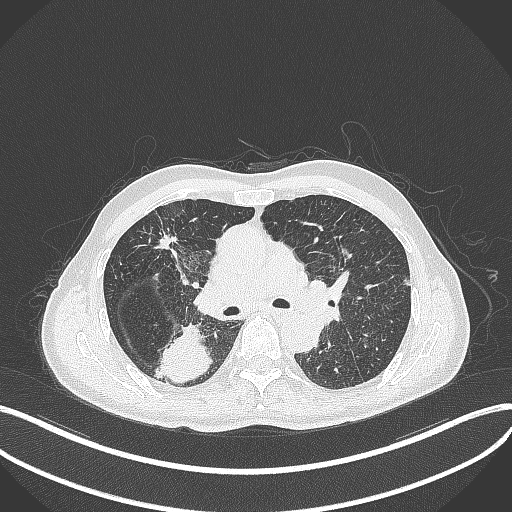
Chest CT, one axial slice. Slice 275 of 428 in the series (ordered by position). Reconstruction kernel B70f. 120 kVp. Lung window (W 1500 / L -600 HU). 512 × 512 image matrix, field of view 400 × 400 mm. Patient: male, 79 years. Case-level facts recorded for this patient, not image findings: clinical TNM (as recorded): T3 N0 M0.
Annotated regions visible in this slice (rectangle marked by the reading radiologist):
- lung tumour (recorded histology: adenocarcinoma): bounding box (x1, y1, x2, y2) in pixels: (157, 321, 215, 383)